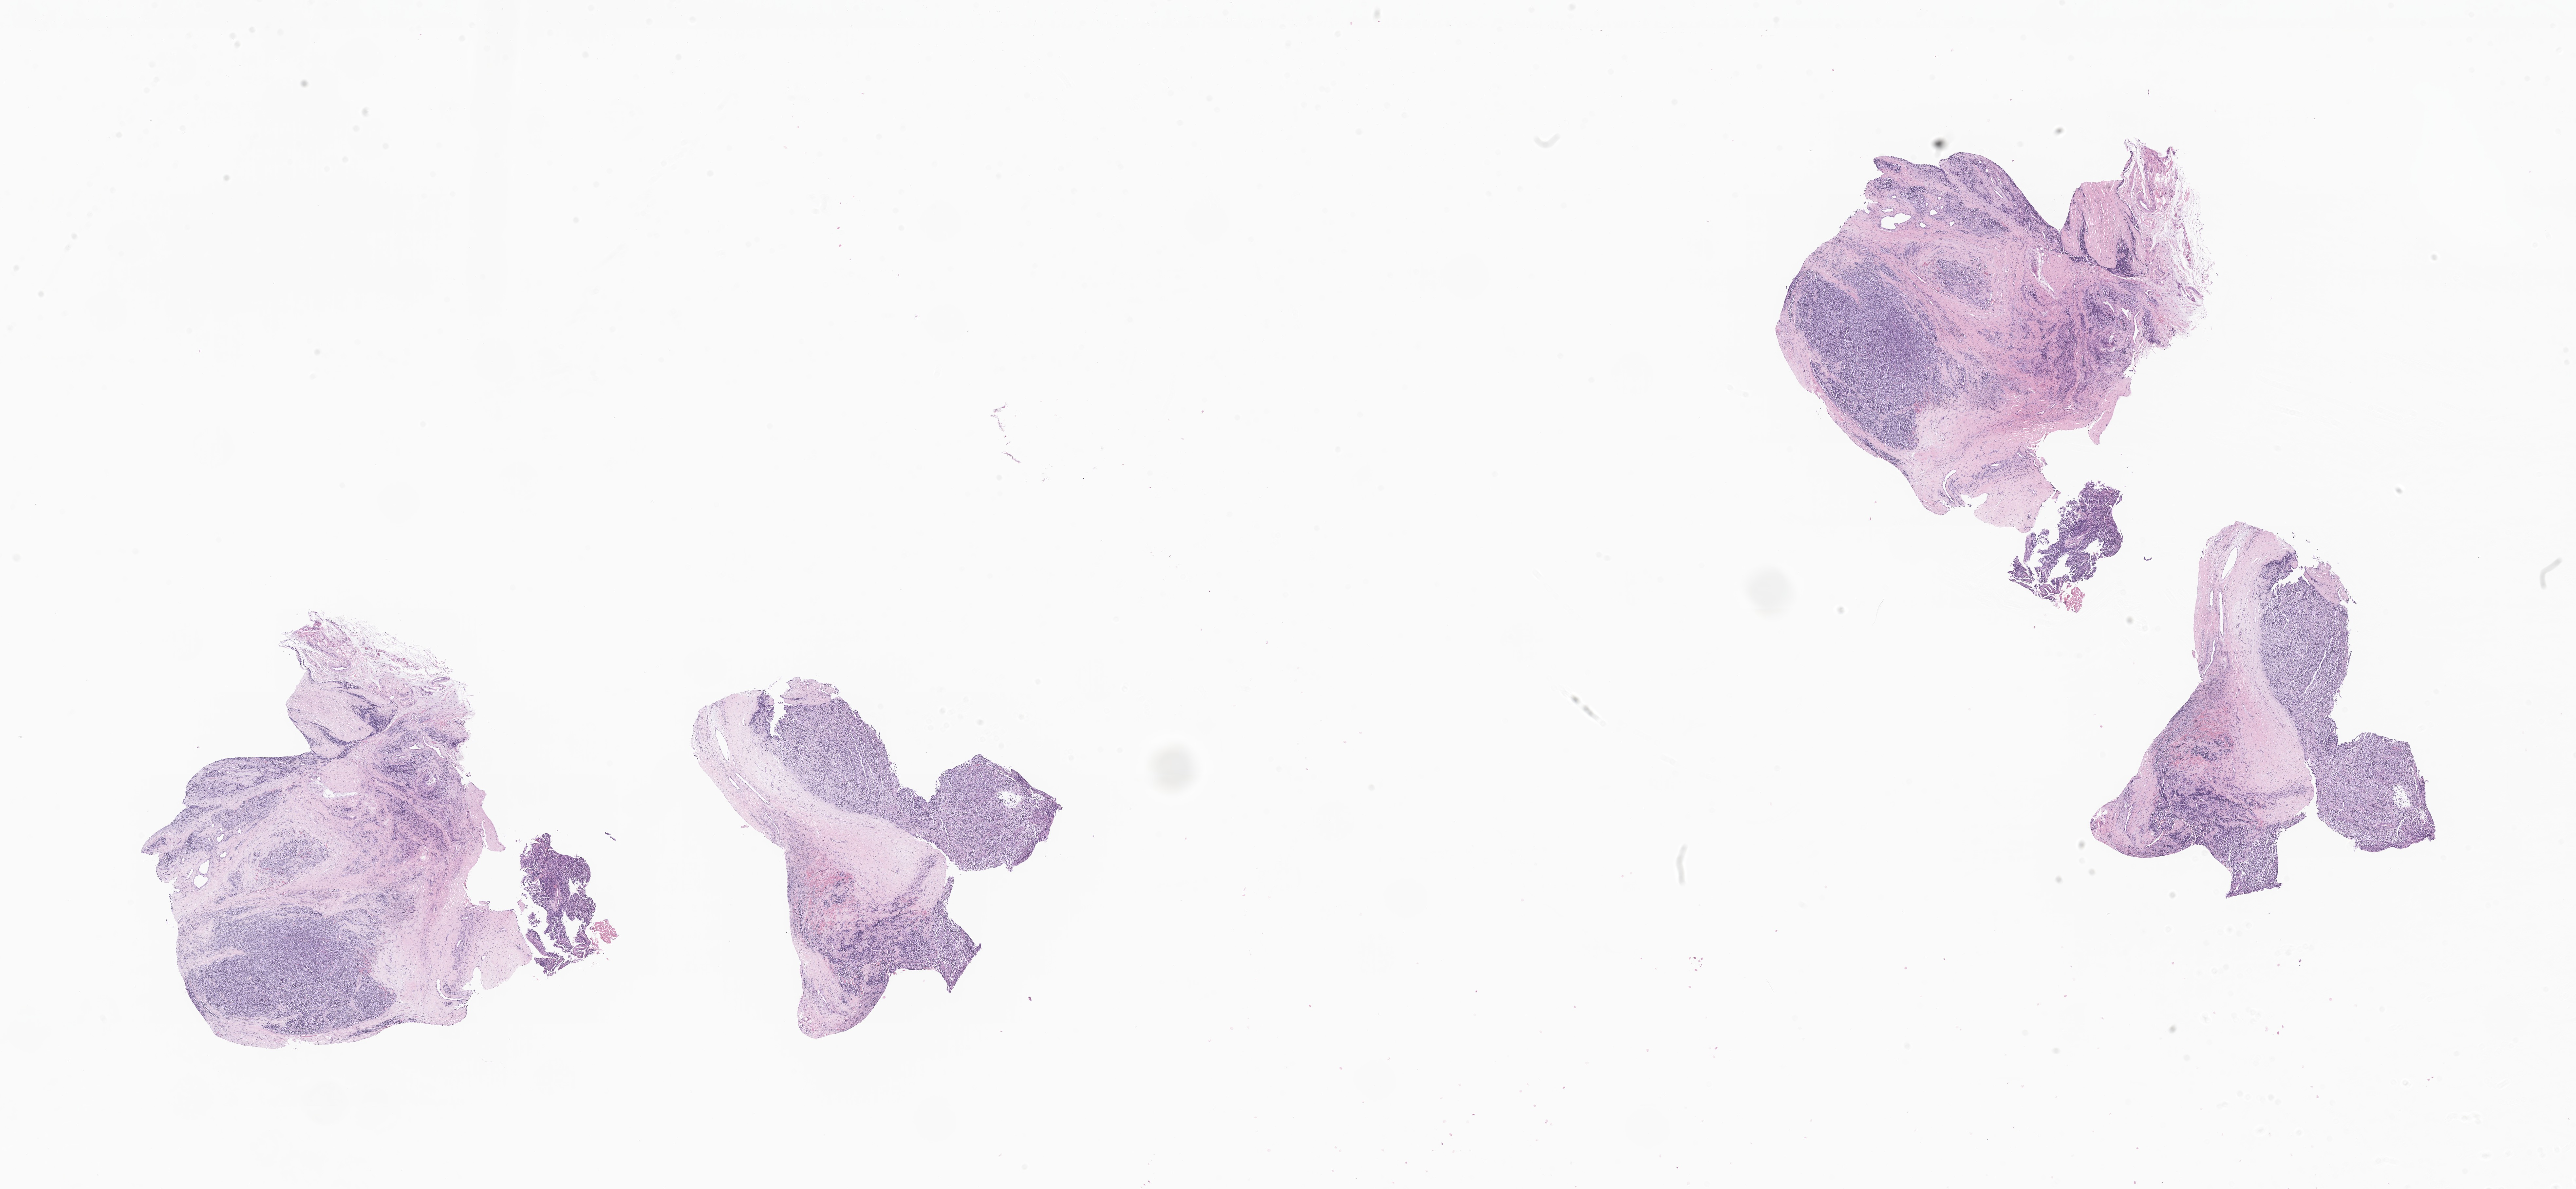
Digitized hematoxylin and eosin (H&E)-stained section of tumor tissue from the lower limb — shown as a low-resolution overview of the whole scanned area (about 33.2 x 15.3 mm). FFPE section. Patient: female, age 53 months.
- recorded diagnosis: Rhabdomyosarcoma, NOS